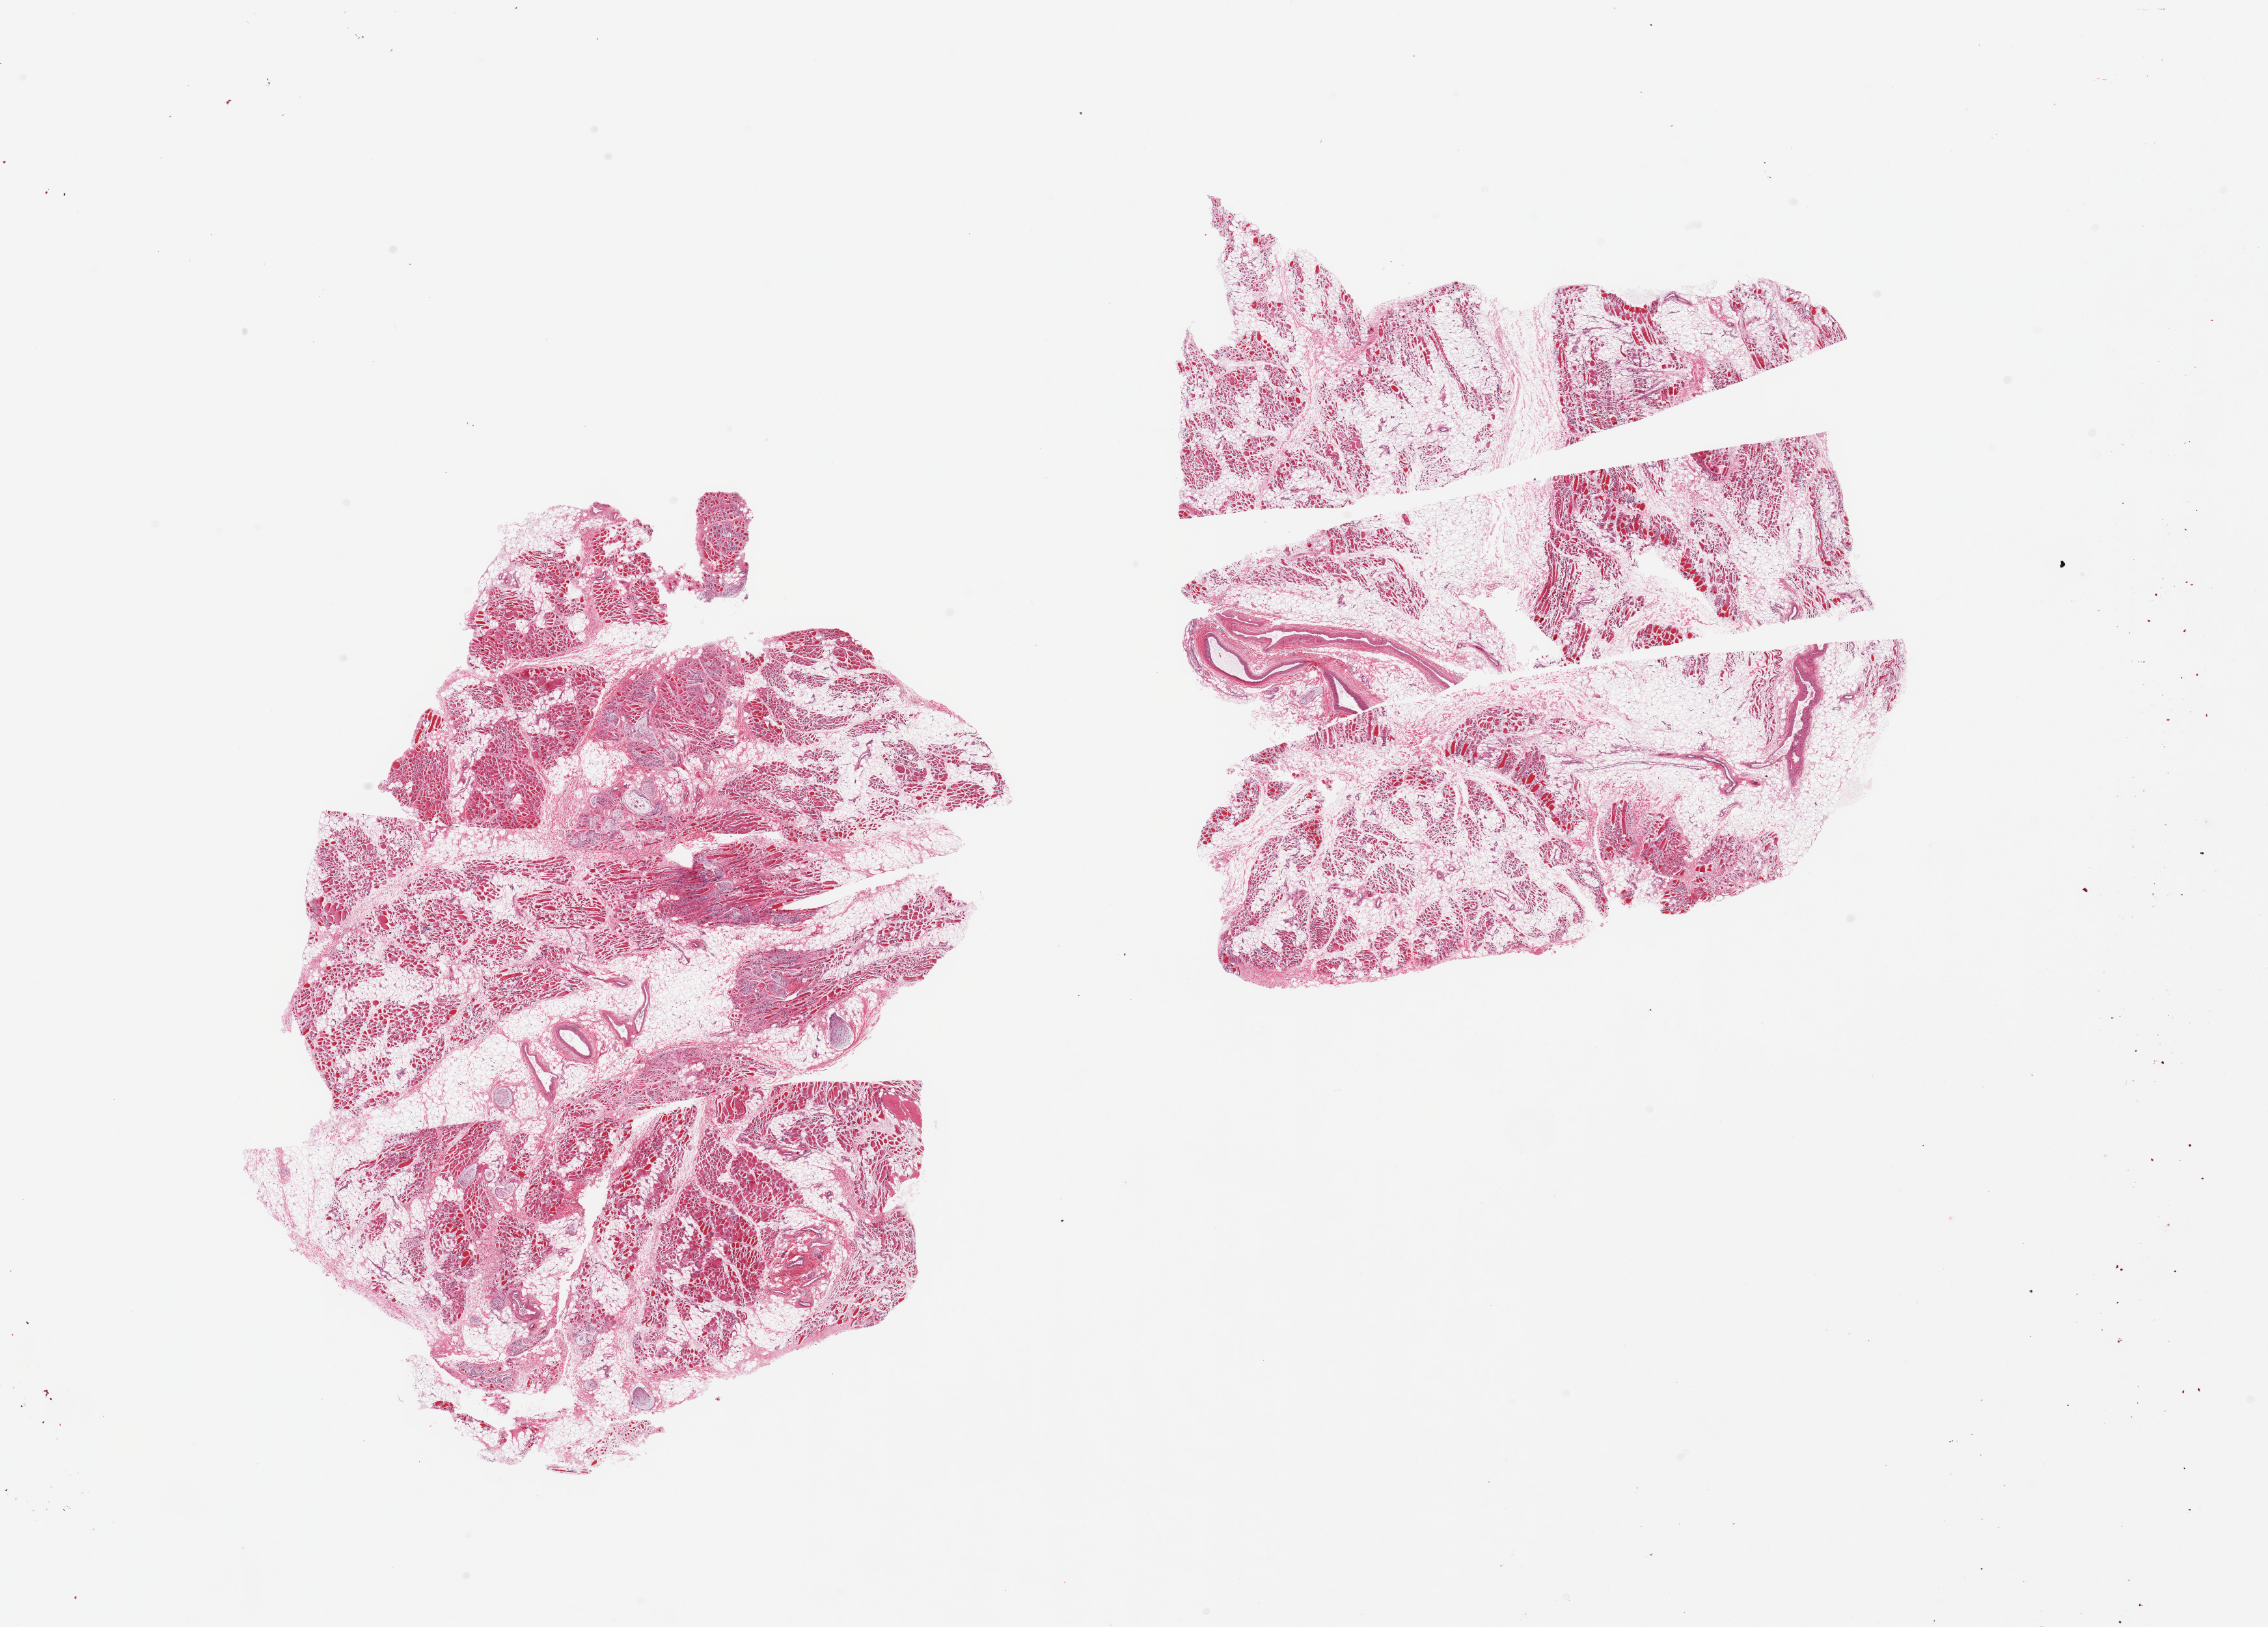
Digitized H&E-stained section — low-resolution overview of the scanned area, about 27.6 x 19.8 mm. PAXgene-fixed, paraffin-embedded tissue. Target tissue: skeletal muscle. Tissue donor sample. Donor: female.
Review note (as recorded): 2 pieces; profound atrophy with subsequent excess of fat/nerve tissue.